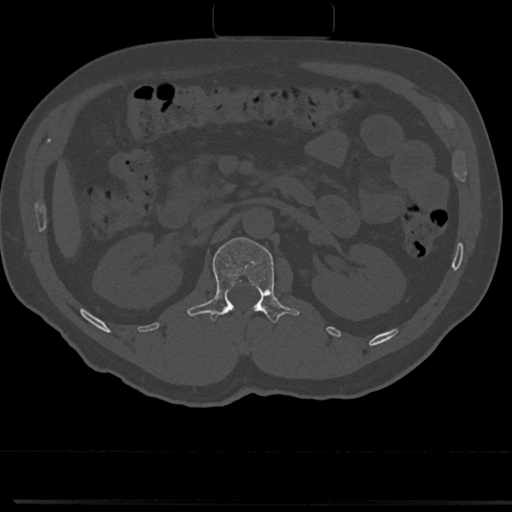
CT including the spine, one axial slice; position 85 of 817 along the scan axis; reconstruction kernel Br40s/3; 120 kVp; bone window (W 1800 / L 400 HU); 0.5 mm slice thickness; 512 × 512 image matrix, field of view 355 × 355 mm. Male patient, age 61 years. From the clinical record (not read from this slice): primary cancer: prostate.
Structures marked on this image (semi-automatic segmentation, software-assisted and operator-edited):
- L1 vertebra: bounding box [x1, y1, x2, y2] px = [191, 238, 297, 324]